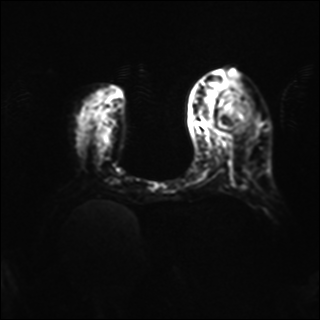
Breast MRI, one axial slice; position 17 of 40 along the scan axis; diffusion-weighted series; image 2 of 4 stored at this slice position (different b-values; order by instance number); 1.5 T; 4 mm slice thickness; 320 × 320 image matrix, field of view 320 × 320 mm. Female patient.
Annotated regions visible in this slice (expert manual segmentation):
- tumour on diffusion-weighted imaging: bounding box [x1, y1, x2, y2] px = [217, 106, 232, 128]